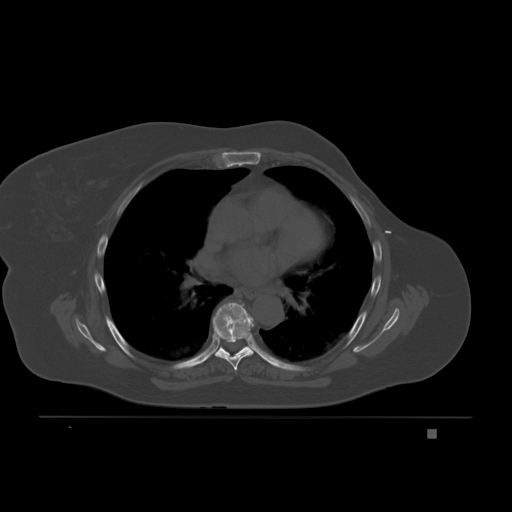
CT including the spine, one axial slice. Position 133 of 221 along the scan axis. Bone window (W 1800 / L 400 HU). 3 mm slice thickness. 512 × 512 image matrix, field of view 474 × 474 mm. Female patient, age 63 years. From the clinical record (not read from this slice): primary cancer: breast.
Outlined on this slice (semi-automatic segmentation, software-assisted and operator-edited):
- T6 vertebra: bounding box (x1, y1, x2, y2) in pixels: (210, 302, 252, 371)
- T7 vertebra: (212, 316, 254, 357)